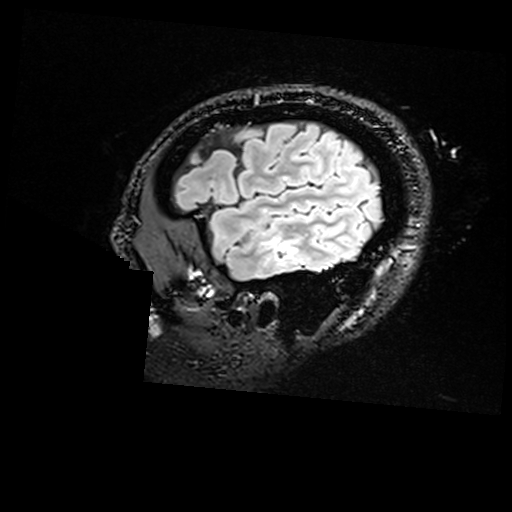
Brain MRI from a brain-tumour surgery series, one sagittal slice. Position 137 of 176 along the scan axis. T2 FLAIR. 1 mm slice thickness. 512 × 512 image matrix. From the clinical record (not read from this slice): histopathology: Non-tumor destructive chronic inflammatory lesion with abnormal vasculature; tumour location: Right Inferior Temporal.
Structures marked on this image (outlined manually by an expert reader):
- residual tumour: bounding box (x1, y1, x2, y2) in pixels: (280, 243, 294, 260)